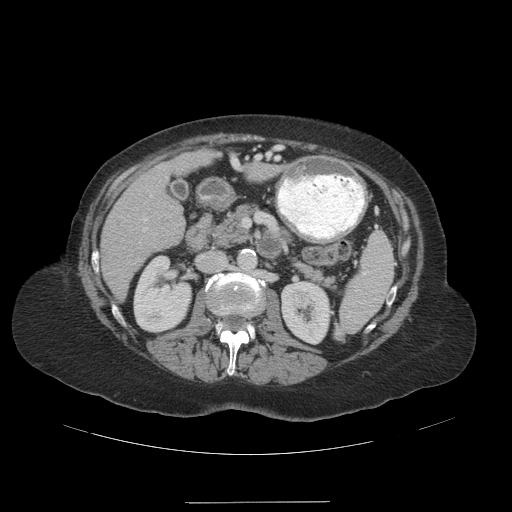
Contrast-enhanced abdominal CT (liver protocol), one axial slice. Position 49 of 99 along the scan axis. Soft-tissue window (W 400 / L 40 HU). 2.5 mm slice thickness. 512 × 512 image matrix, field of view 440 × 440 mm. Case-level facts recorded for this patient, not image findings: diagnosis: hepatocellular carcinoma (patient treated with transarterial chemoembolisation; whether this scan precedes or follows treatment is not stated here); TNM stage (as recorded): Stage-IVA; Child-Pugh class: A; tumour nodularity: multinodular.
Outlined on this slice (semi-automatically segmented with operator editing):
- liver parenchyma outside the tumour (the mass and vessels are separate outlines, so this box may not span the whole liver): bounding box [x1, y1, x2, y2] px = [100, 150, 215, 298]
- liver vessels: [143, 218, 147, 221]